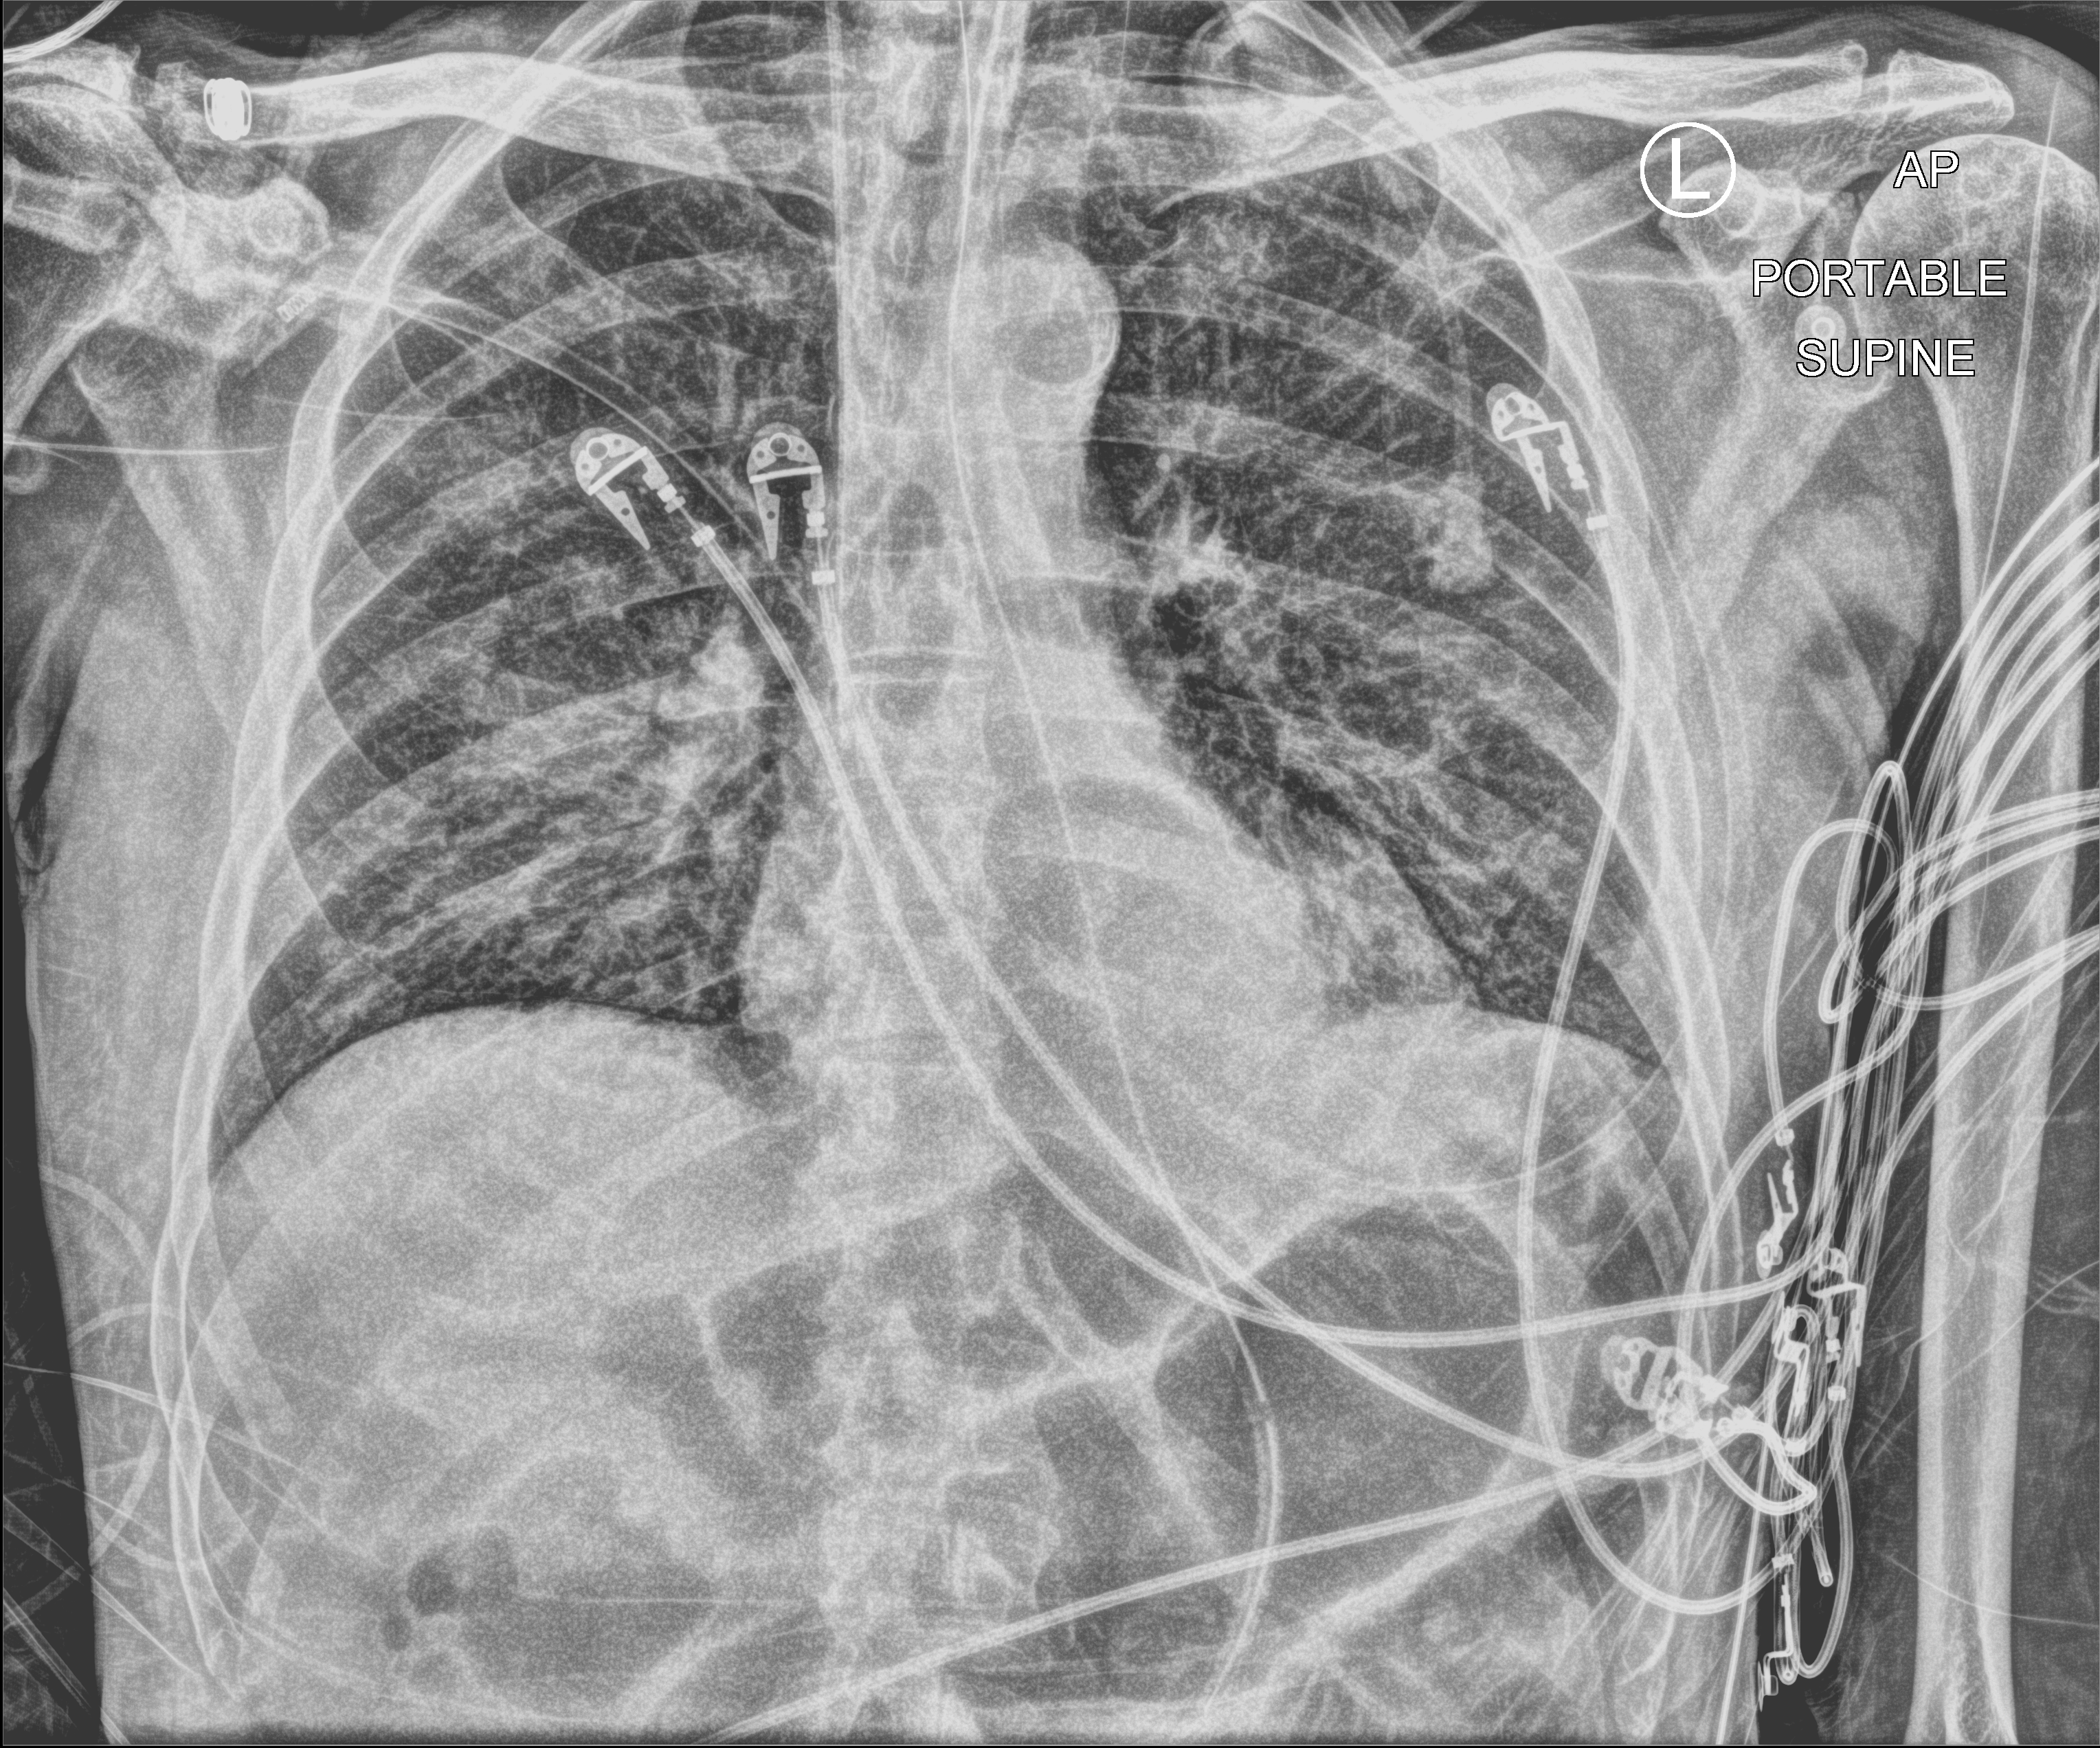
Portable chest radiograph; anteroposterior (AP) projection. Male patient hospitalised with COVID-19, age 75–90 years.
From the hospital-stay record, not from the radiograph (when in the stay this image was taken is not recorded): mechanically ventilated during this hospital stay: yes; admitted to intensive care during this hospital stay: yes; chronic kidney disease (admission record): no.